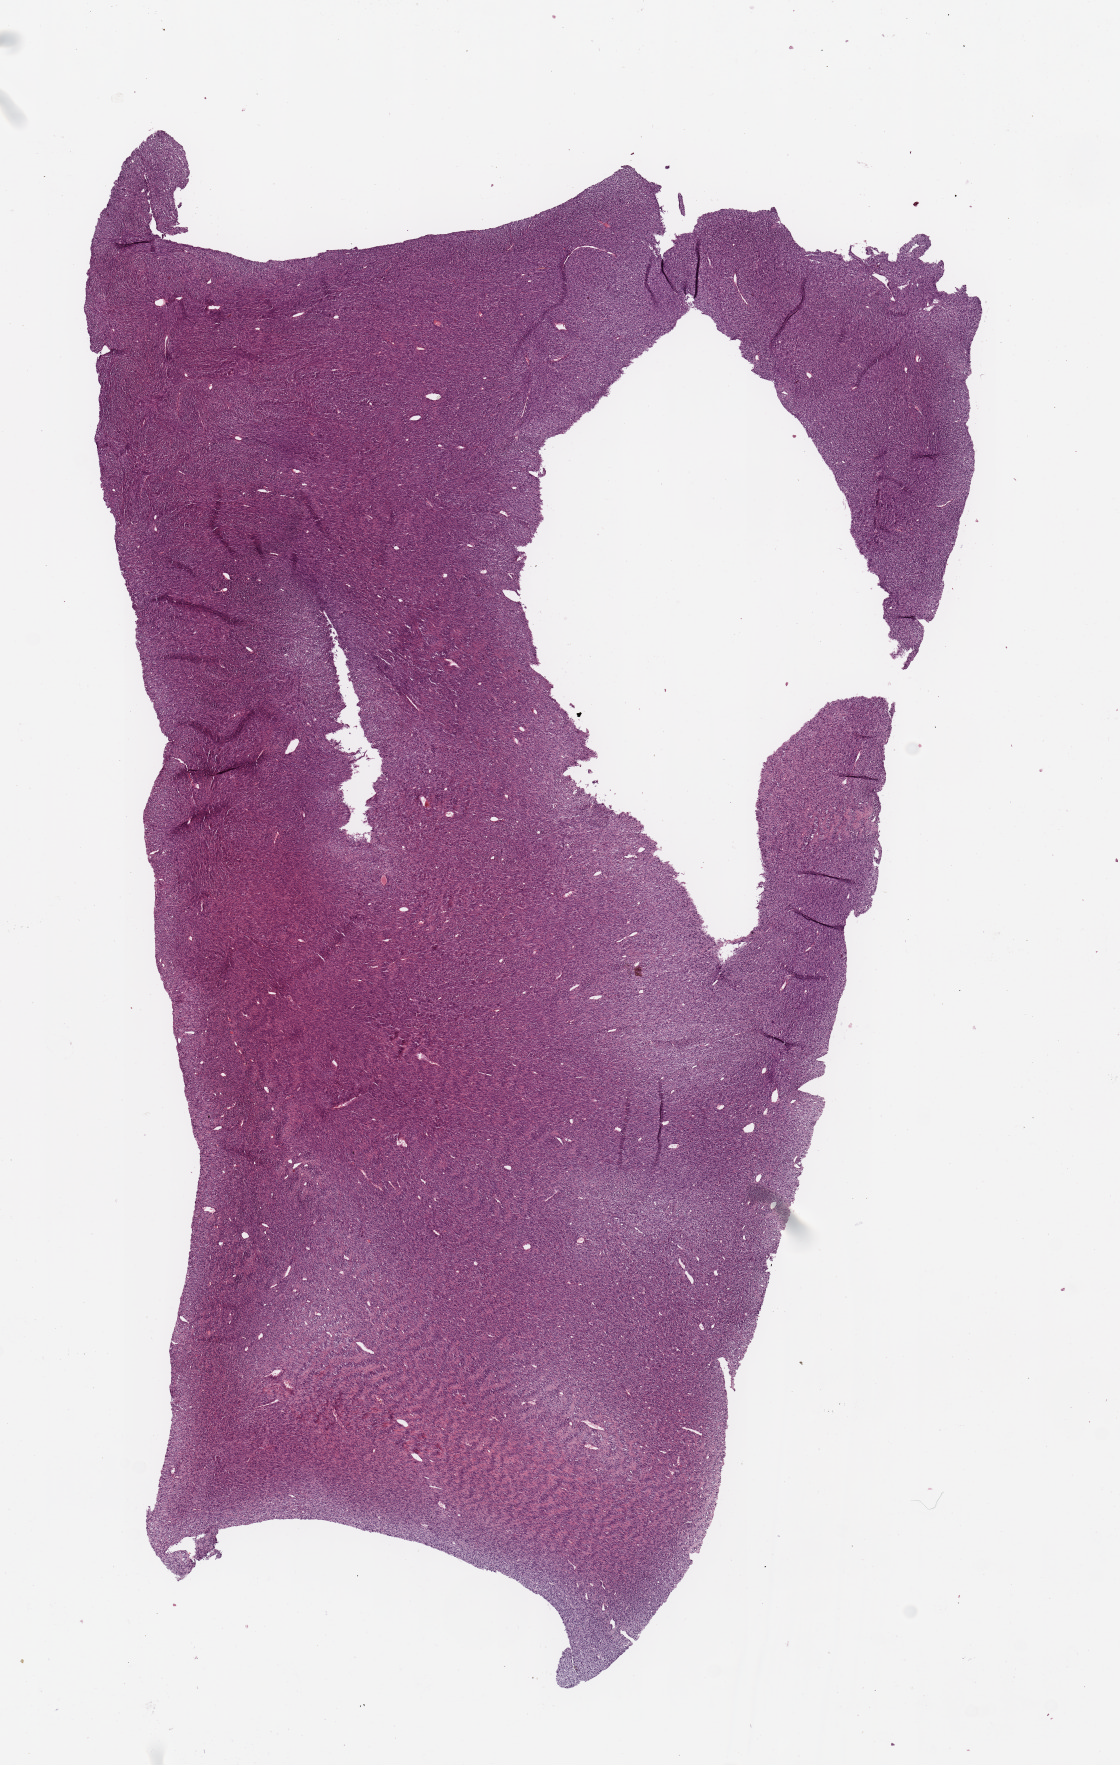
Hematoxylin and eosin (H&E) stained whole-slide image — whole scanned area (about 8.9 x 14.0 mm, acquisition: 20x scan) shown as a low-resolution overview. Tumour tissue sample. Patient: female, age 43 years.
Patient diagnosis (cohort enrolment): sarcoma (site not recorded at cohort level). Primary tumour site (as recorded): lower extremity.